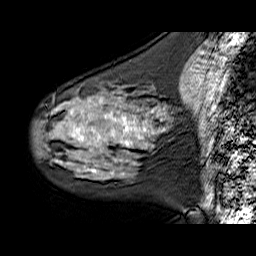
Breast MRI (dynamic contrast-enhanced), one sagittal slice; position 21 of 60 along the scan axis; dynamic contrast-enhanced series, time point 2 of 6 at this slice position (early post-contrast); 1.5 T; TE 6.3 ms, TR 32.9 ms; 4 mm slice thickness; 256 × 256 image matrix, field of view 200 × 200 mm. Female patient. Case-level facts recorded for this patient, not image findings: setting: breast cancer imaged before/during neoadjuvant chemotherapy; receptor status: HER2-positive.
Outlined on this slice (semi-automatically segmented with operator editing):
- analysis volume of interest (the breast-tissue region the enhancement analysis was run in; not a lesion): bounding box <34,84,172,180> (left, top, right, bottom; pixels)
- tumour enhancement mask (voxels above the 100 % enhancement threshold inside the analysis volume of interest): <73,113,146,172>